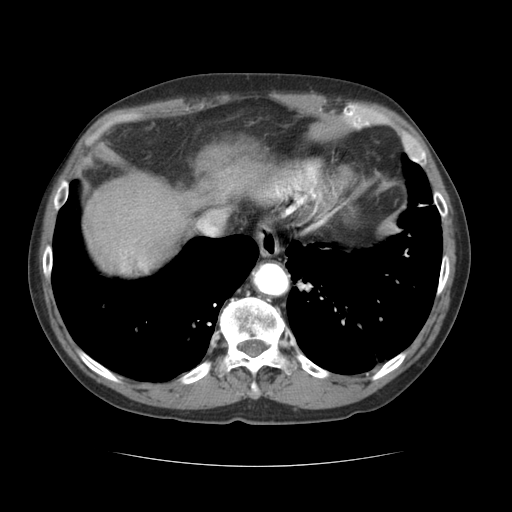
Contrast-enhanced abdominal CT (liver protocol), one axial slice; position 57 of 69 along the scan axis; 120 kVp; soft-tissue window (W 400 / L 40 HU); 2.5 mm slice thickness; 512 × 512 image matrix. From the clinical record (not read from this slice): diagnosis: hepatocellular carcinoma (patient treated with transarterial chemoembolisation; whether this scan precedes or follows treatment is not stated here); TNM stage (as recorded): Stage-II; Child-Pugh class: B.
Annotated regions visible in this slice (semi-automatically segmented with operator editing):
- abdominal aorta: bounding box <255,265,287,294> (left, top, right, bottom; pixels)
- liver parenchyma outside the tumour (the mass and vessels are separate outlines, so this box may not span the whole liver): <84,148,258,272>
- mass: <119,248,153,278>